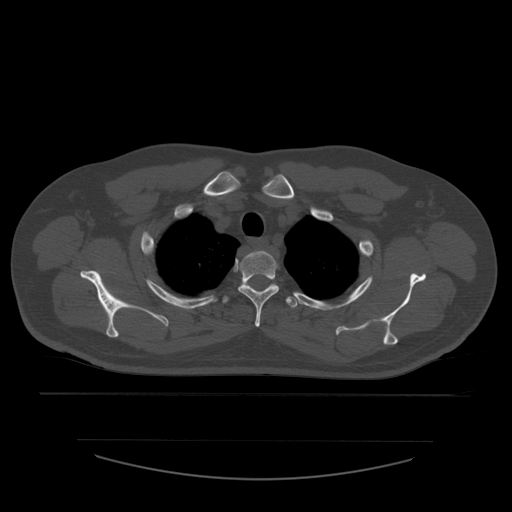
CT including the spine, one axial slice. Reconstruction kernel STANDARD. Bone window (W 1800 / L 400 HU). 1.25 mm slice thickness. 512 × 512 image matrix. Patient age 44 years. From the clinical record (not read from this slice): primary cancer: soft tissue sarcoma.
Structures marked on this image (semi-automatic segmentation, software-assisted and operator-edited):
- T2 vertebra: bounding box <239,251,280,327> (left, top, right, bottom; pixels)
- T3 vertebra: <223,297,298,308>